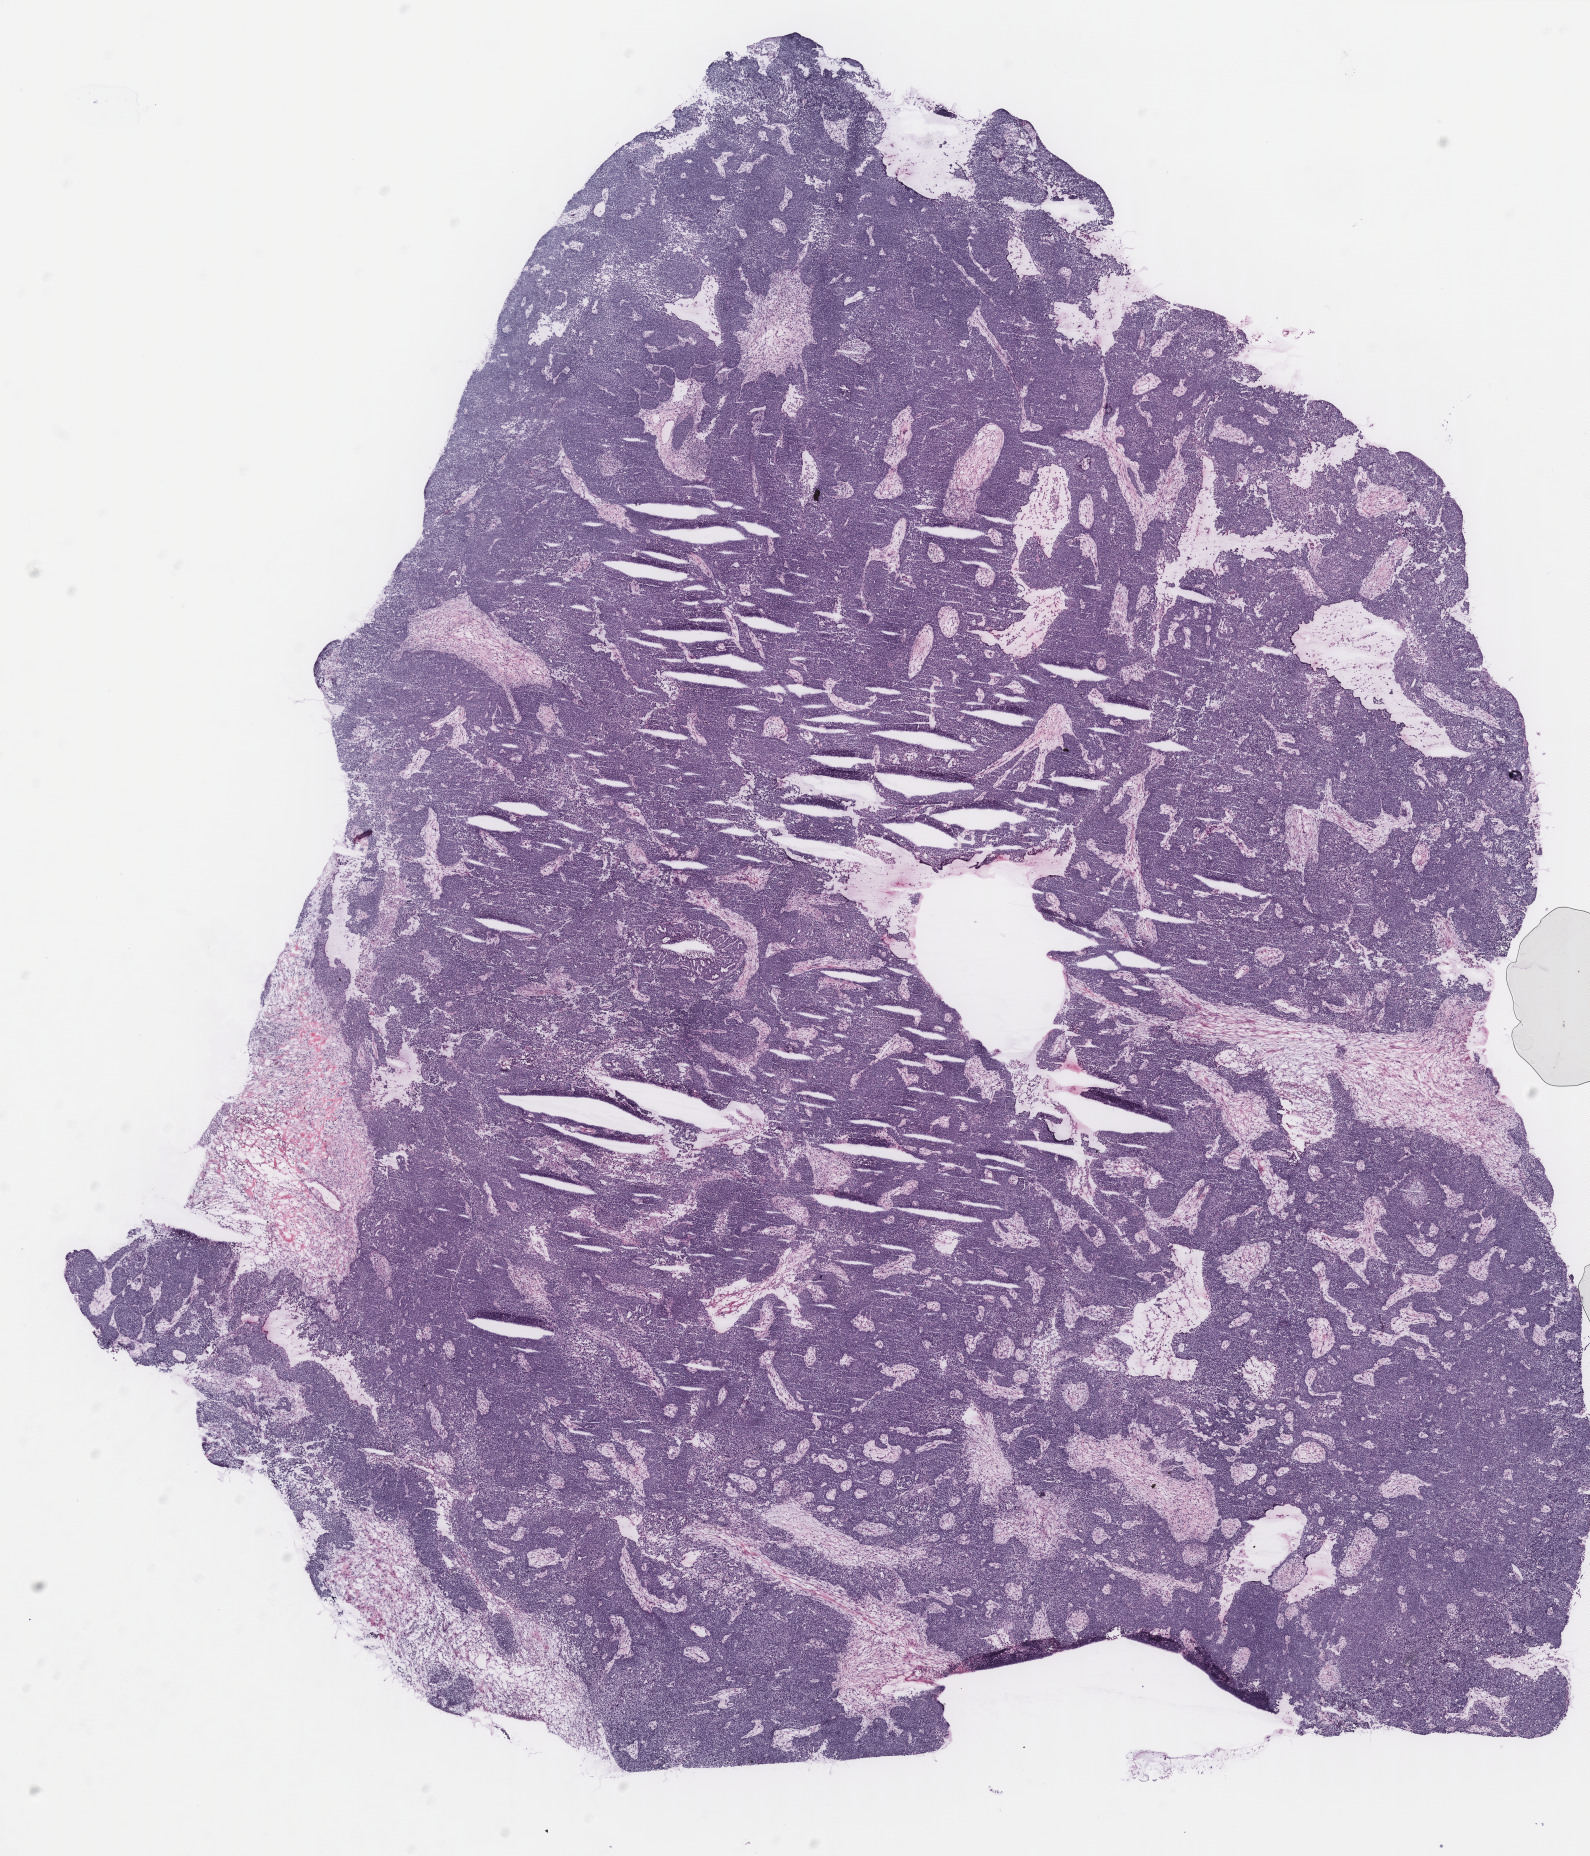
Whole-slide histology image, H&E, a low-resolution overview of the entire scanned area, about 12.7 x 14.9 mm (from a 40x scan), ovary, tumour tissue. 54-year-old female patient.
- primary tumour site (as recorded): peritoneum
- histologic diagnosis: Serous adenocarcinoma, NOS (peritoneum, NOS)